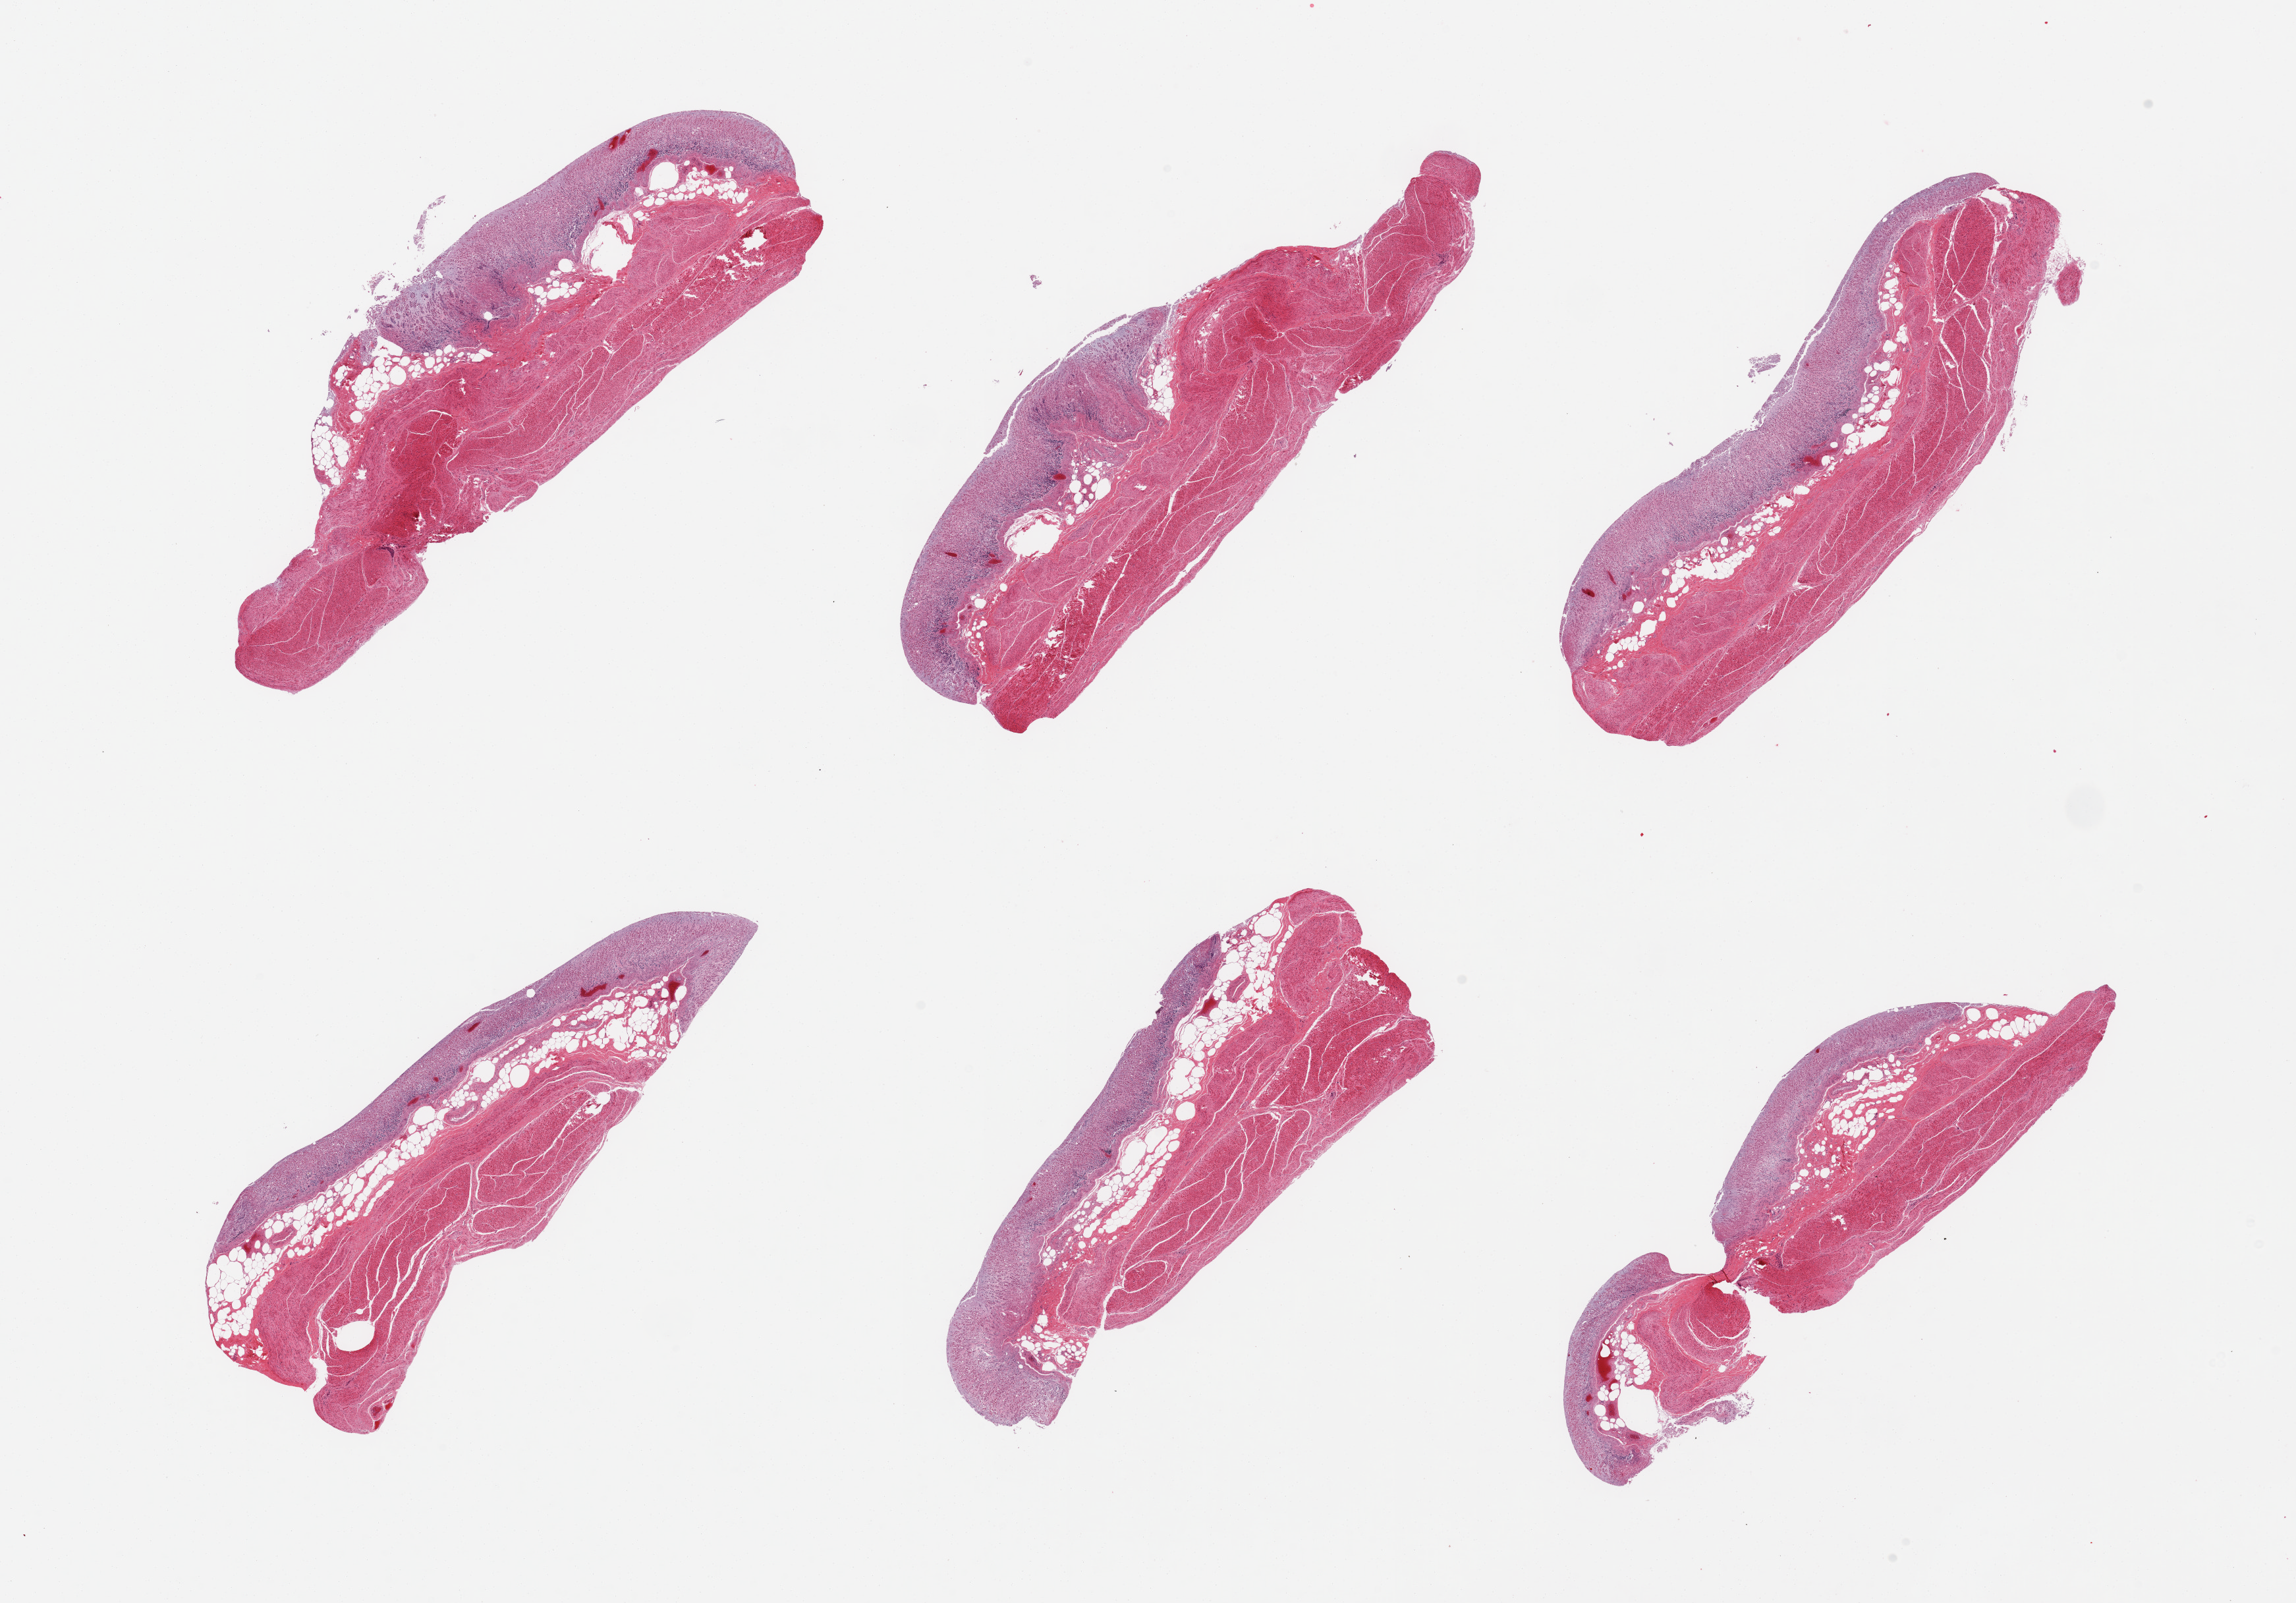
H&E whole-slide image, low-resolution overview of the scanned area, about 27.6 x 19.2 mm (from a 20x scan), PAXgene-fixed paraffin-embedded (PFPE) section, target tissue: stomach, donor tissue sample. Donor sex: male.
* pathologist's review note for this sample: 6 pieces; full thickness sections, mucosa is severely autolyzed